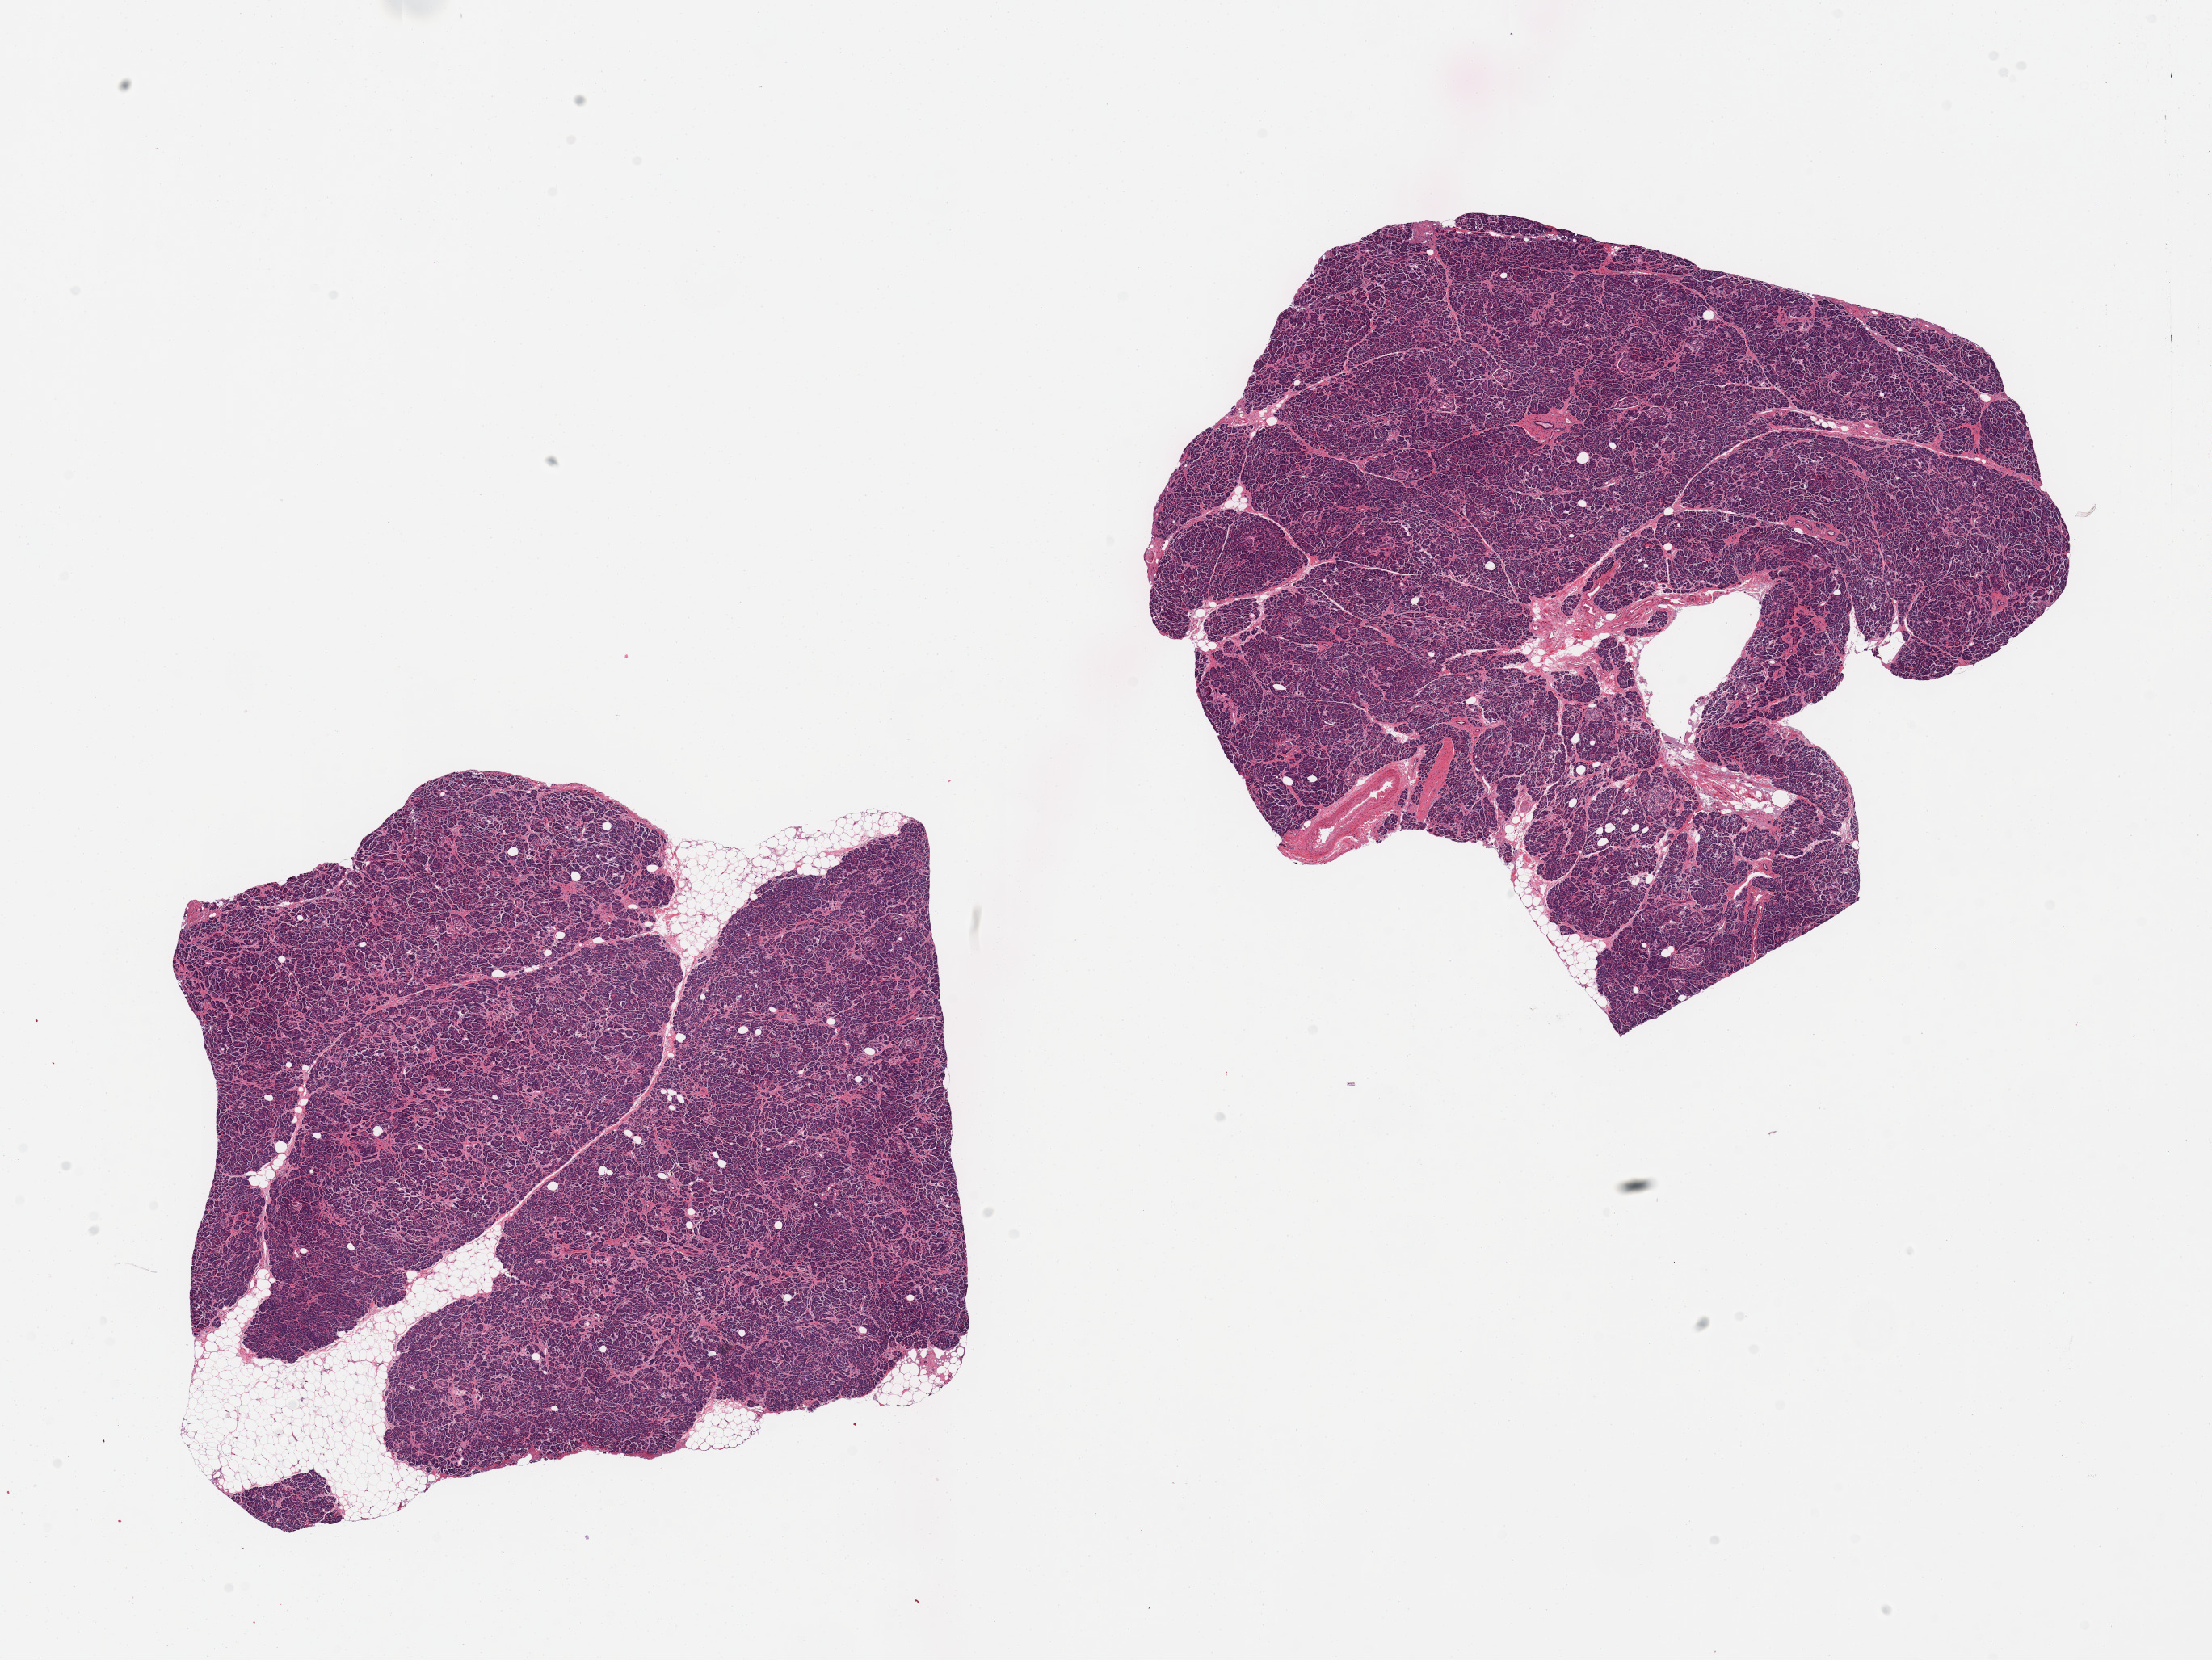
Whole-slide image, haematoxylin and eosin stain — low-resolution overview of the scanned area, about 21.7 x 16.3 mm (slide scanned at 20x). PAXgene-fixed paraffin-embedded (PFPE) section. Target tissue: pancreas. Tissue donor sample. Donor sex: male.
Pathologist's review note for this sample: 2 pieces well trimmed; scattered well preserved Langerhans islands; <10% externall fat.